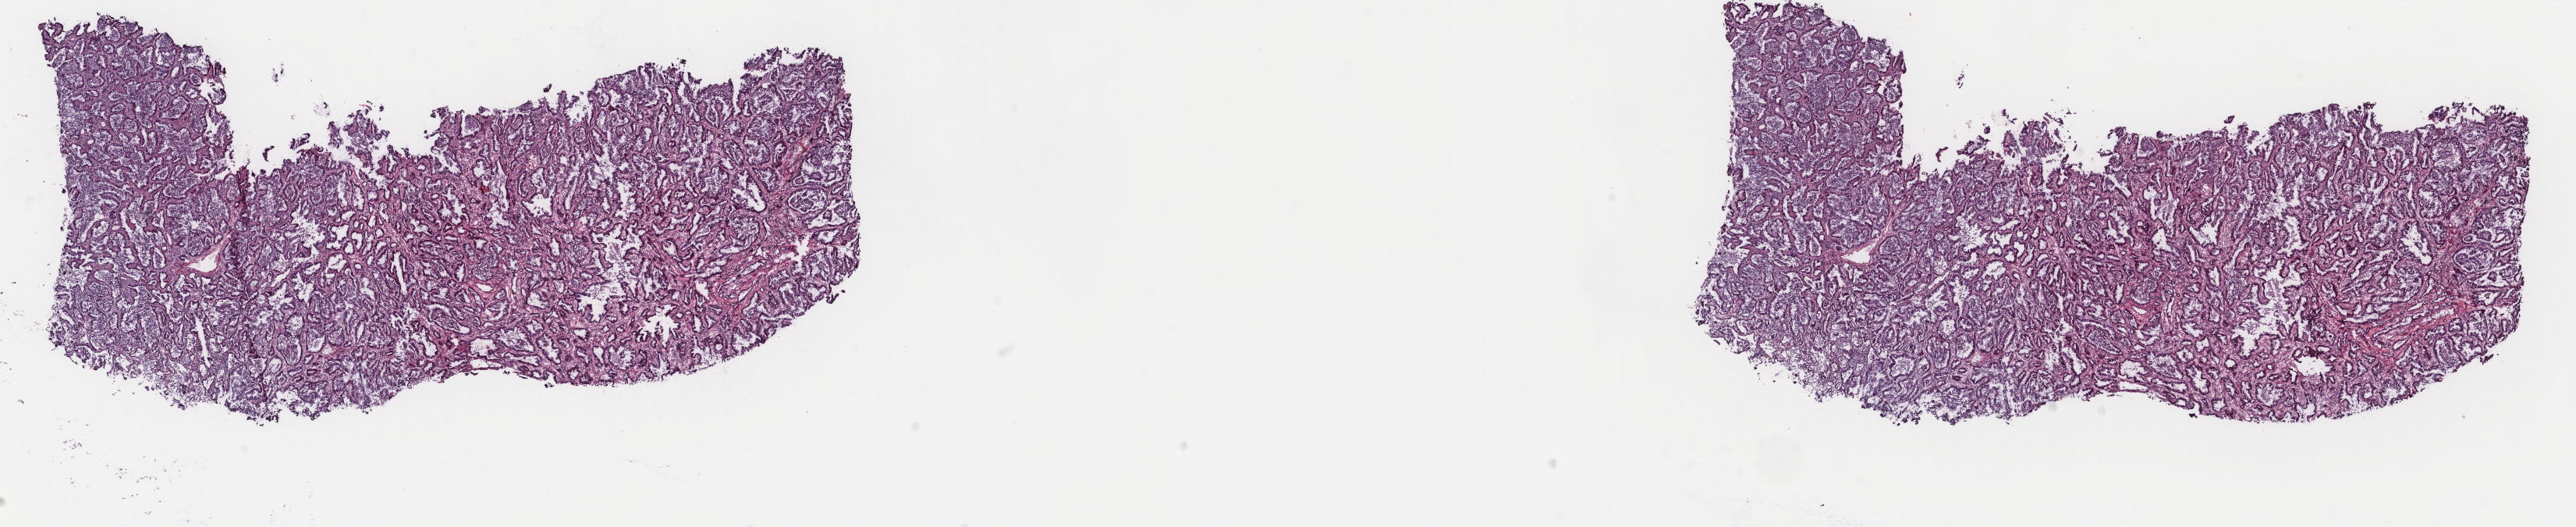
Whole-slide histology image, H&E, whole scanned area (about 26.2 x 5.4 mm, from a 40x scan) shown as a low-resolution overview. Frozen section. Lung, primary tumour sample. Male, age 75 years at initial diagnosis. Composition of this section per pathologist review: tumour cells 70%, tumour nuclei 100%, normal cells 0%, stromal cells 30%, necrosis 0%. Inflammatory infiltration, as recorded: lymphocyte infiltration 3%, monocyte infiltration 5%, neutrophil infiltration 0%.
TNM: T1b N1 MX. Histologic diagnosis: Adenocarcinoma with mixed subtypes (lower lobe, lung). Laterality: left. AJCC pathologic stage: IIA (7th edition).